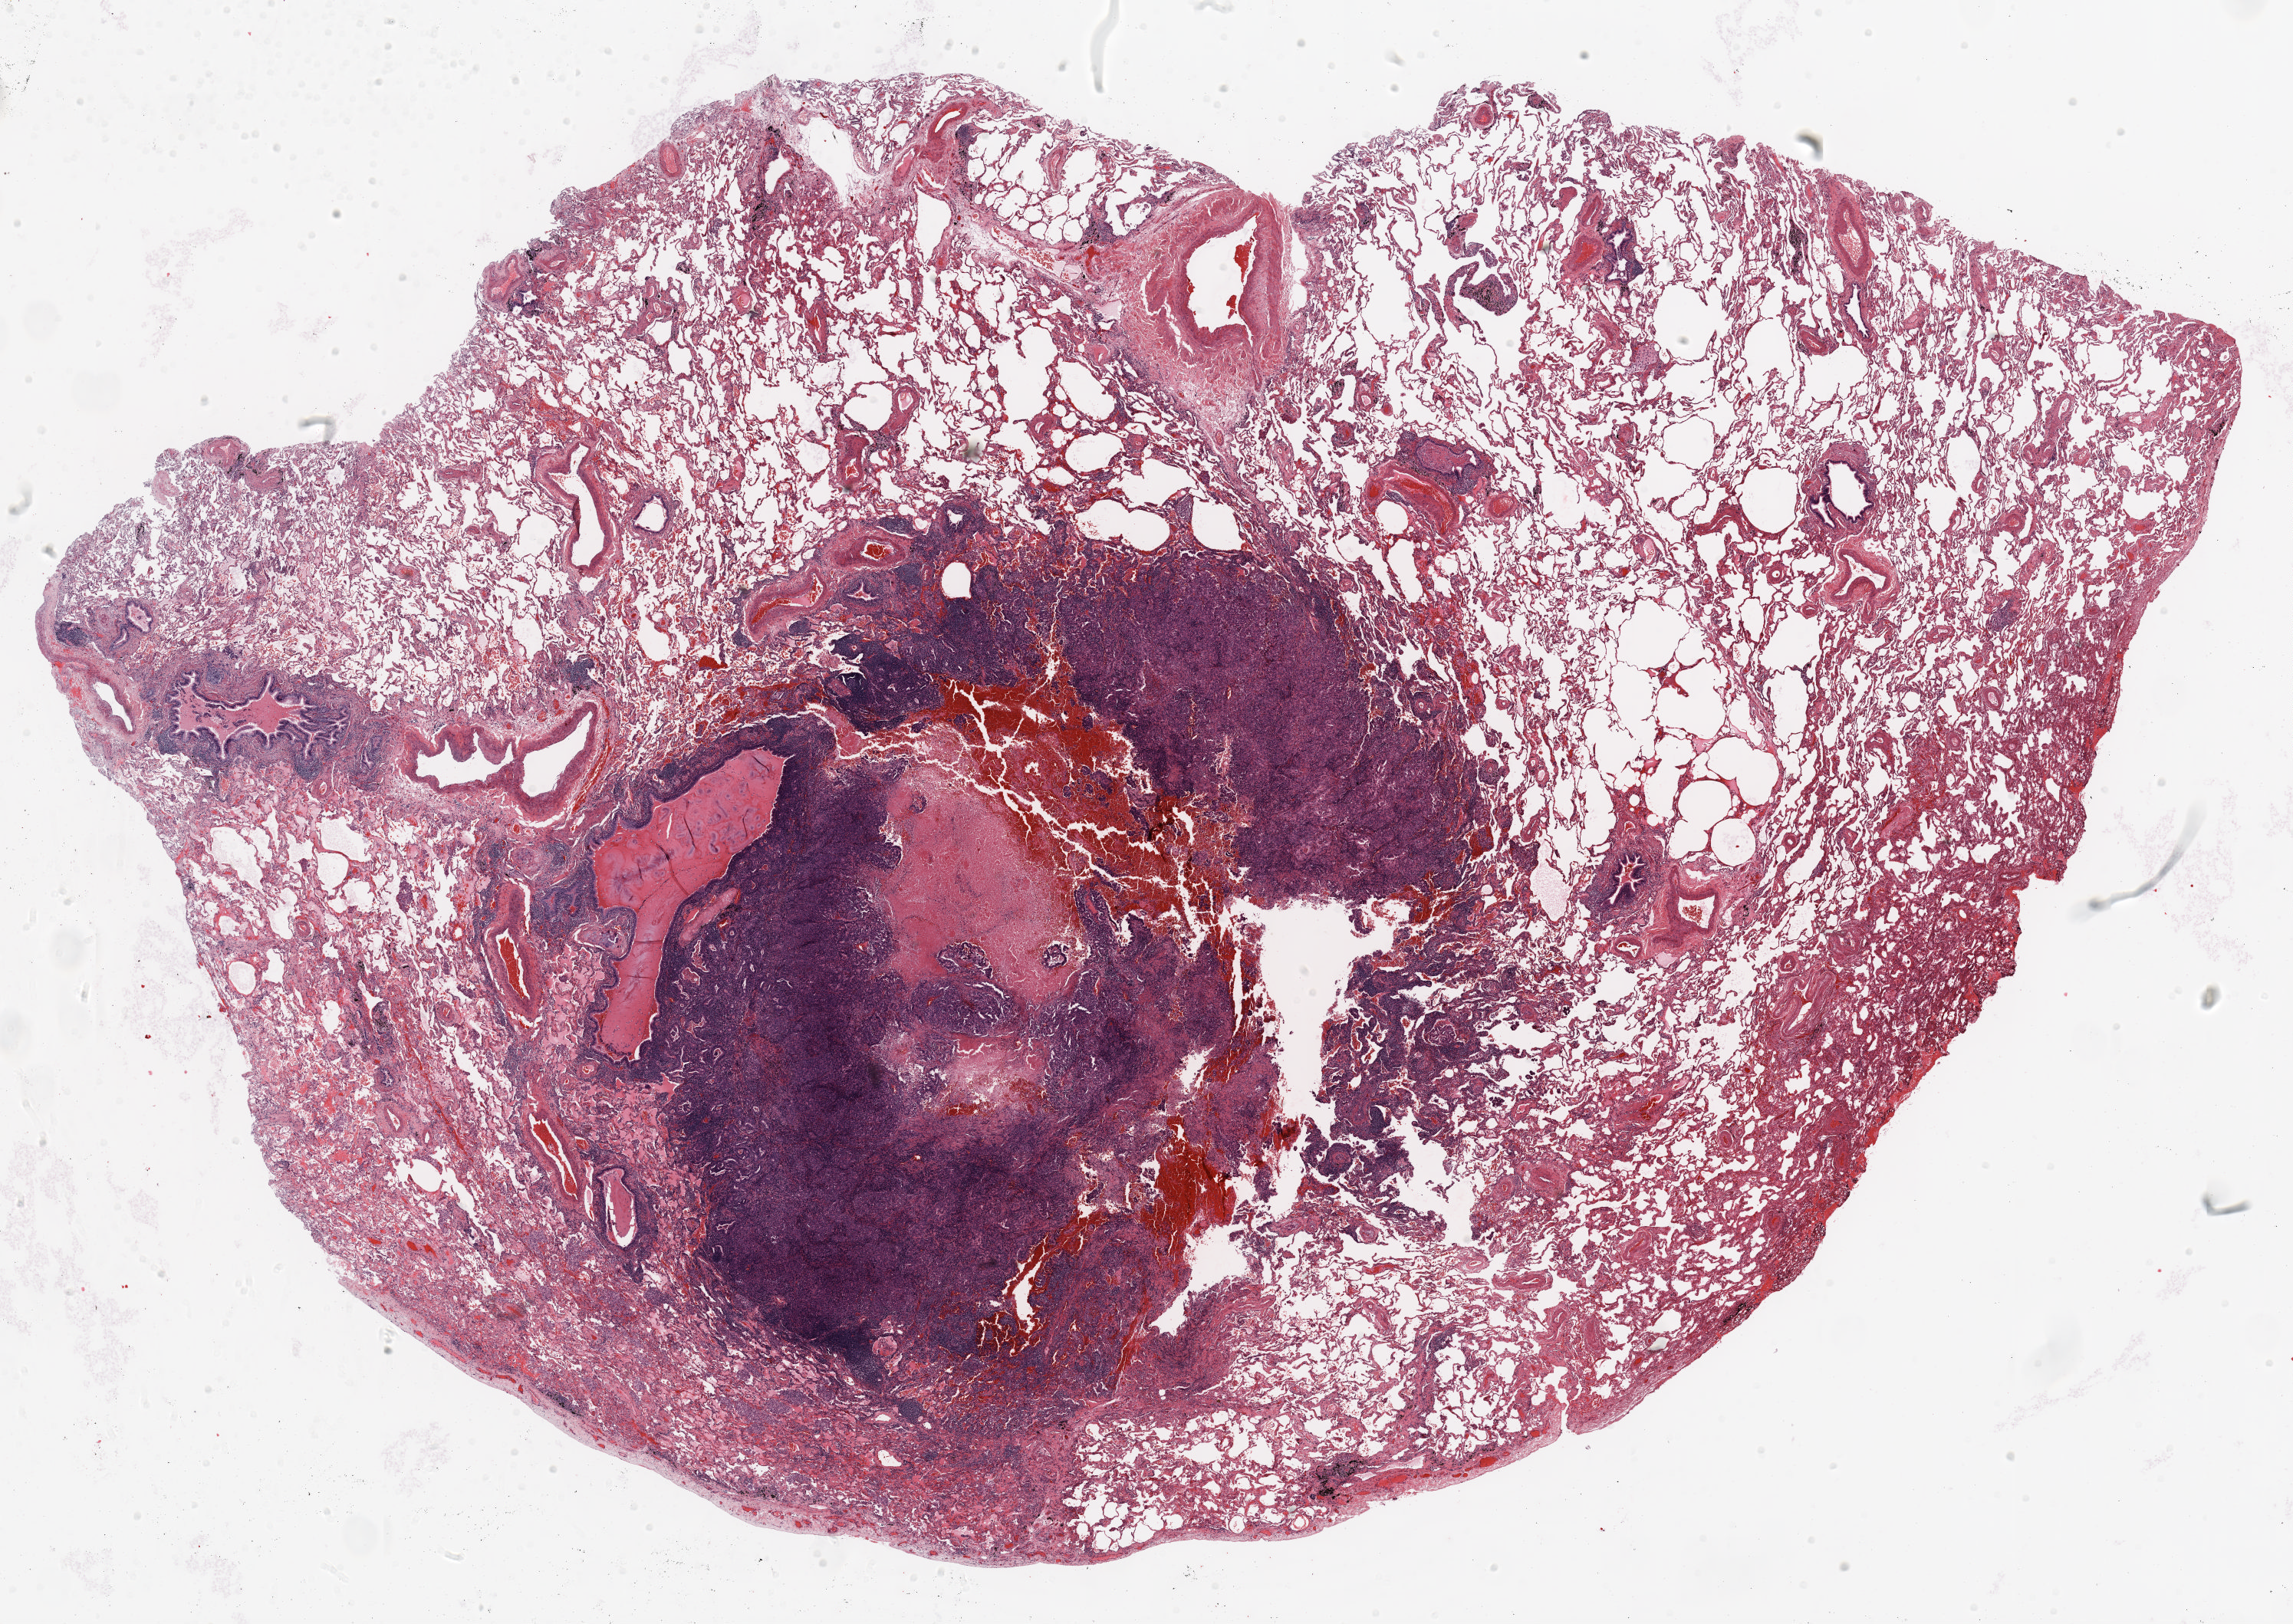
Whole-slide histology image, H&E, whole scanned area (about 24.0 x 17.0 mm) shown as a low-resolution overview; formalin-fixed paraffin-embedded (FFPE) section; lung tissue. Female, age 72 at enrolment. Former smoker at enrolment. Grade: moderately differentiated (G2).
Primary tumour location (clinical record): right upper lobe. Stage (AJCC 6th edition): IA. Participant's lung-cancer diagnosis: Adenocarcinoma, NOS. Tumour size (pathology): 15 mm.